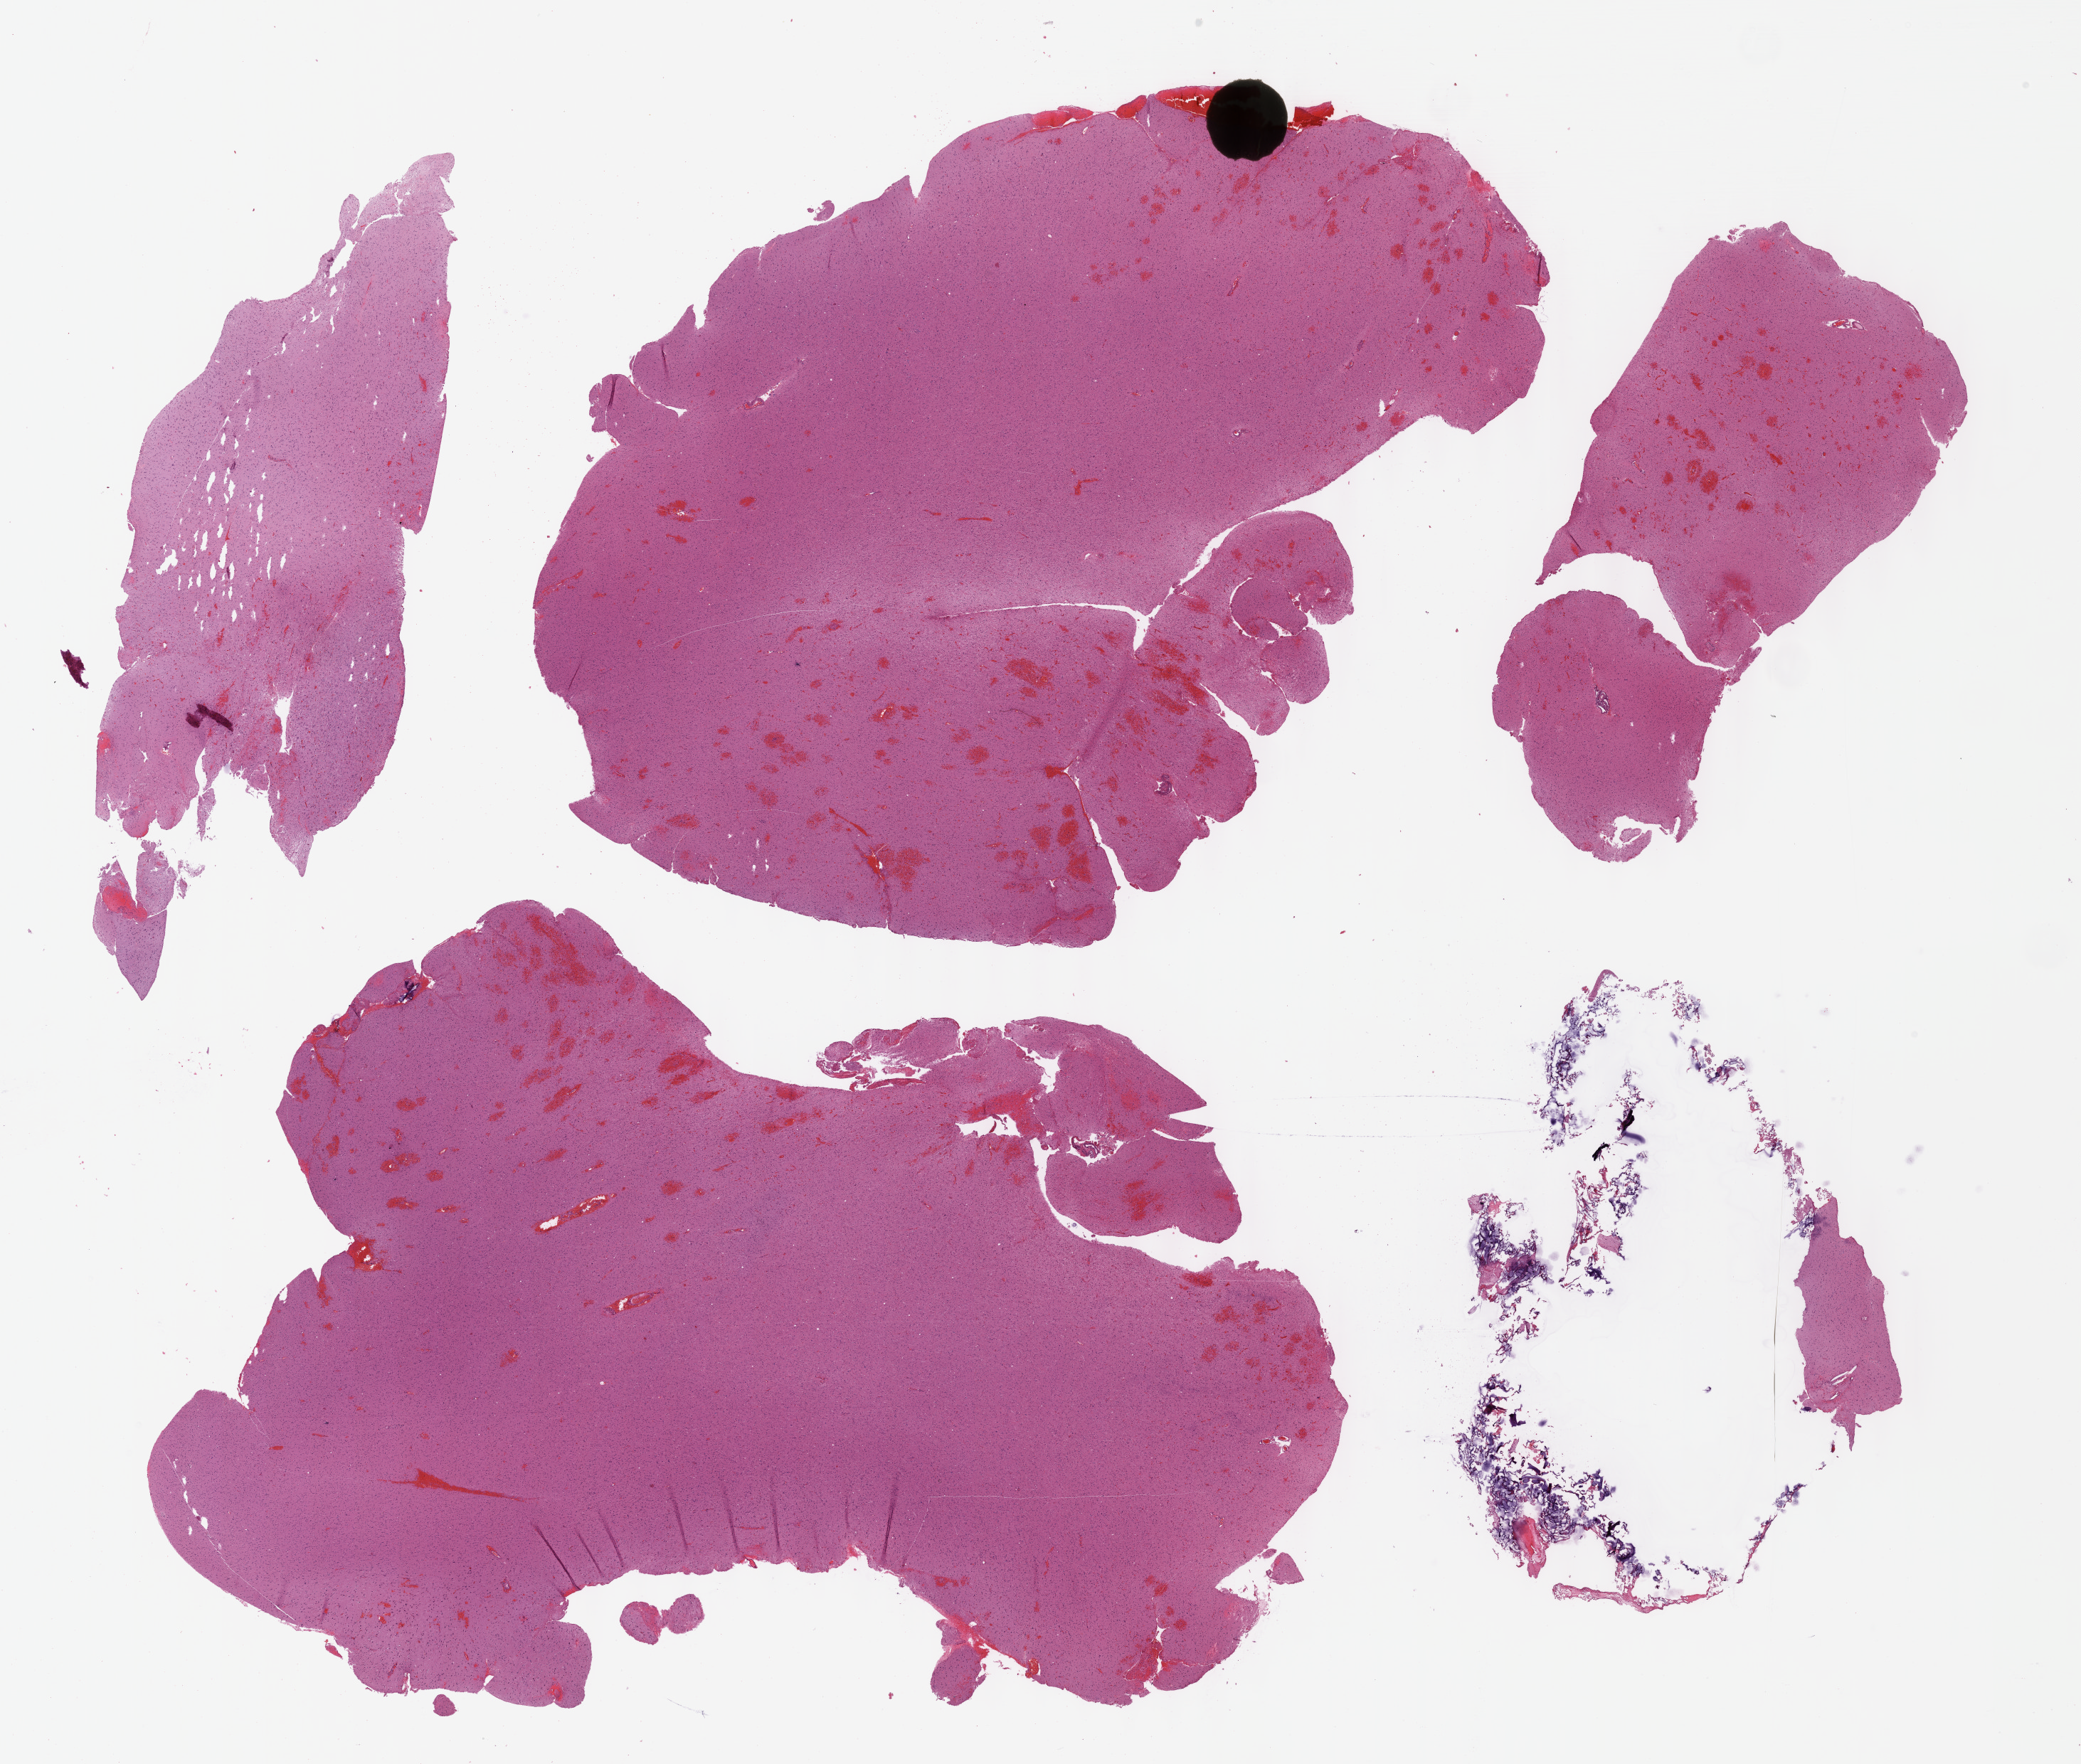
Whole-slide histology image, Hematoxylin and eosin (H&E) stained, low-resolution overview of the scanned area, about 23.6 x 20.0 mm (slide scanned at 40x). Formalin-fixed paraffin-embedded (FFPE) diagnostic section. Sample: primary tumour, brain. Patient: female, age at initial diagnosis 64 years. Histologic grade: G2 (moderately differentiated).
• diagnosis: Oligodendroglioma, NOS (cerebrum)
• laterality: right